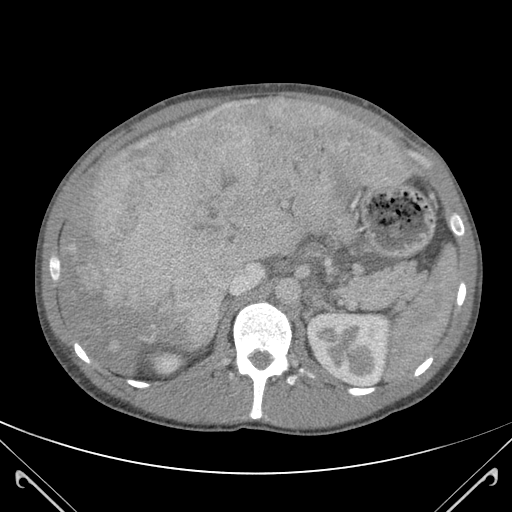
Contrast-enhanced abdominal CT (liver protocol), one axial slice; slice 73 of 118 in the series (ordered by position); 120 kVp; soft-tissue window (W 400 / L 40 HU); 3 mm slice thickness; 512 × 512 image matrix, field of view 380 × 380 mm. From the clinical record (not read from this slice): diagnosis: hepatocellular carcinoma (patient treated with transarterial chemoembolisation; whether this scan precedes or follows treatment is not stated here); TNM stage (as recorded): Stage-IIIB; Child-Pugh class: A; tumour nodularity: uninodular.
Annotated regions visible in this slice (semi-automatically segmented with operator editing):
- abdominal aorta: bounding box <276,279,298,304> (left, top, right, bottom; pixels)
- liver parenchyma outside the tumour (the mass and vessels are separate outlines, so this box may not span the whole liver): <58,99,415,375>
- mass: <64,99,406,348>
- liver vessels: <193,100,391,295>